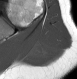
MRI of an extremity soft-tissue mass, one axial slice. Position 18 of 28 along the scan axis. MR volume resampled by the dataset authors to the PET/CT grid (not the native acquisition matrix). 3.27 mm slice thickness. 77 × 79 image matrix, field of view 75 × 77 mm. Female patient. Case-level facts recorded for this patient, not image findings: histological type: malignant fibrous histiocytoma; grade: low; site of the primary tumour: left arm.
Annotated regions visible in this slice (expert contour drawn on MRI and transferred to this co-registered scan by the dataset authors):
- gross tumour volume (mass): box from (x=28, y=41) to (x=50, y=58) px